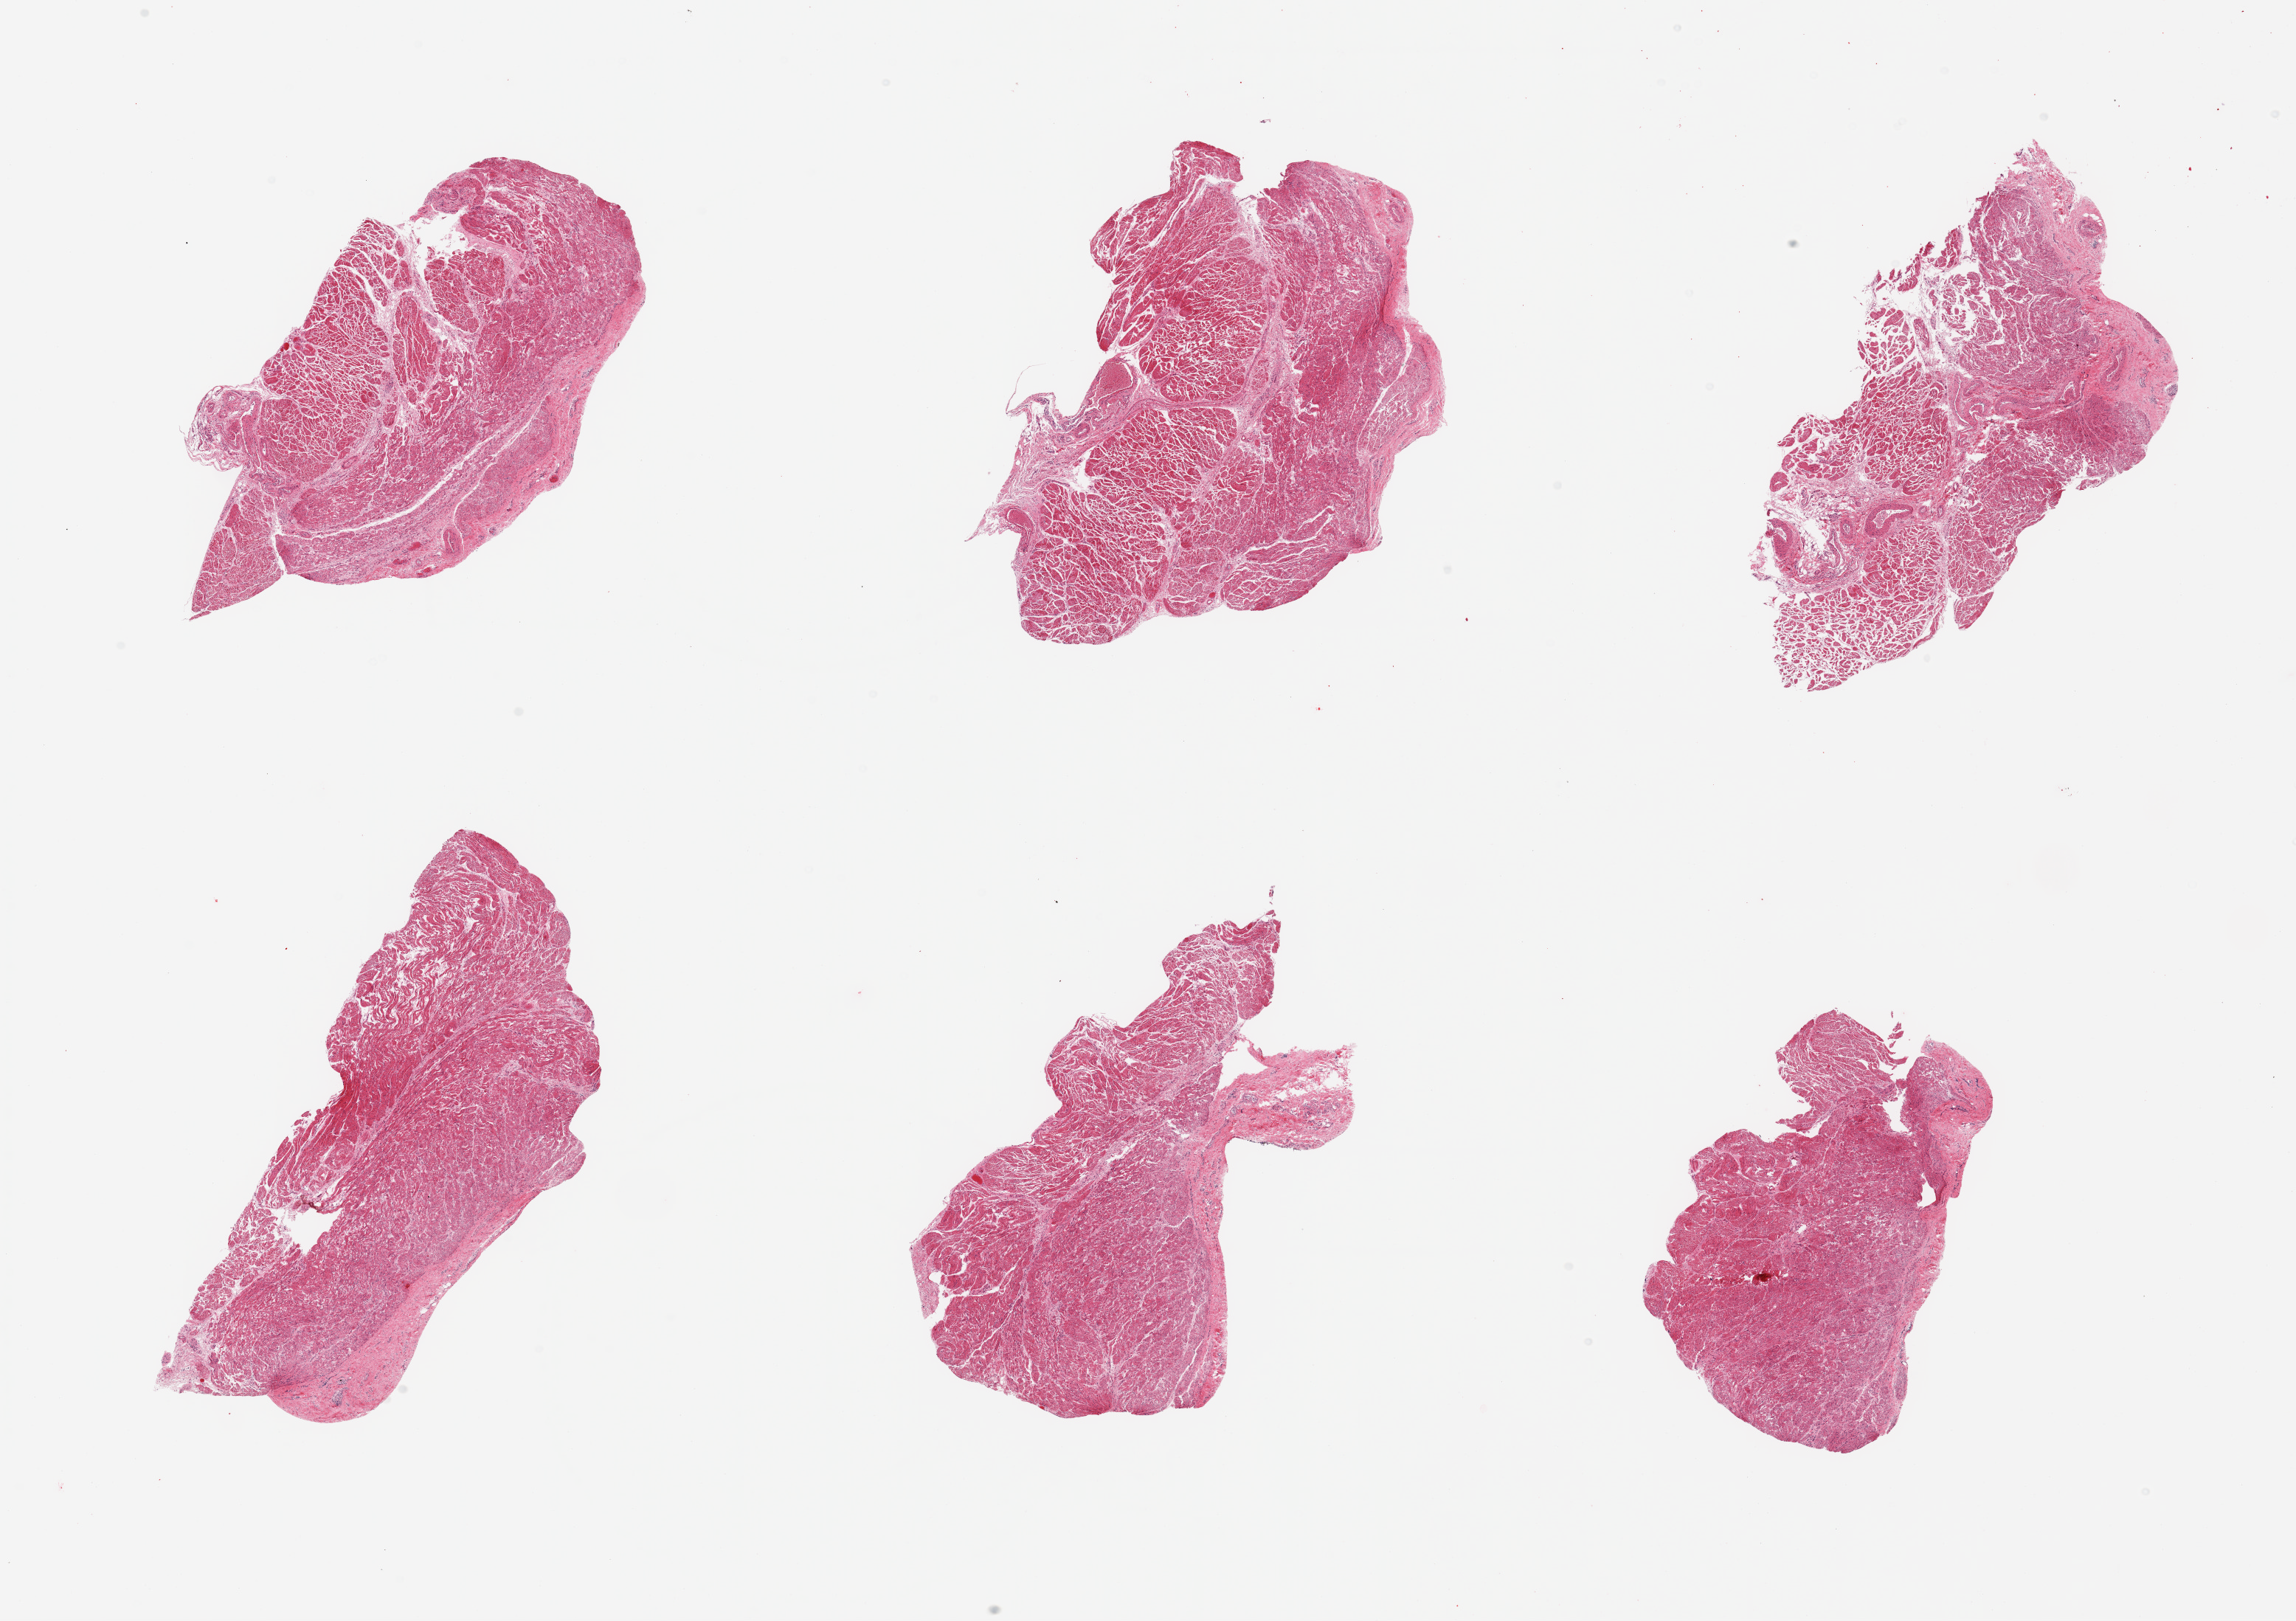
Whole-slide image, haematoxylin and eosin stain — shown as a low-resolution overview of the whole scanned area (about 24.6 x 17.4 mm); PAXgene-fixed, paraffin-embedded tissue; section of gastroesophageal junction (target tissue); donor tissue sample. Donor: male.
* reviewer comment on this tissue sample: 6 pieces, confirmed target muscularis